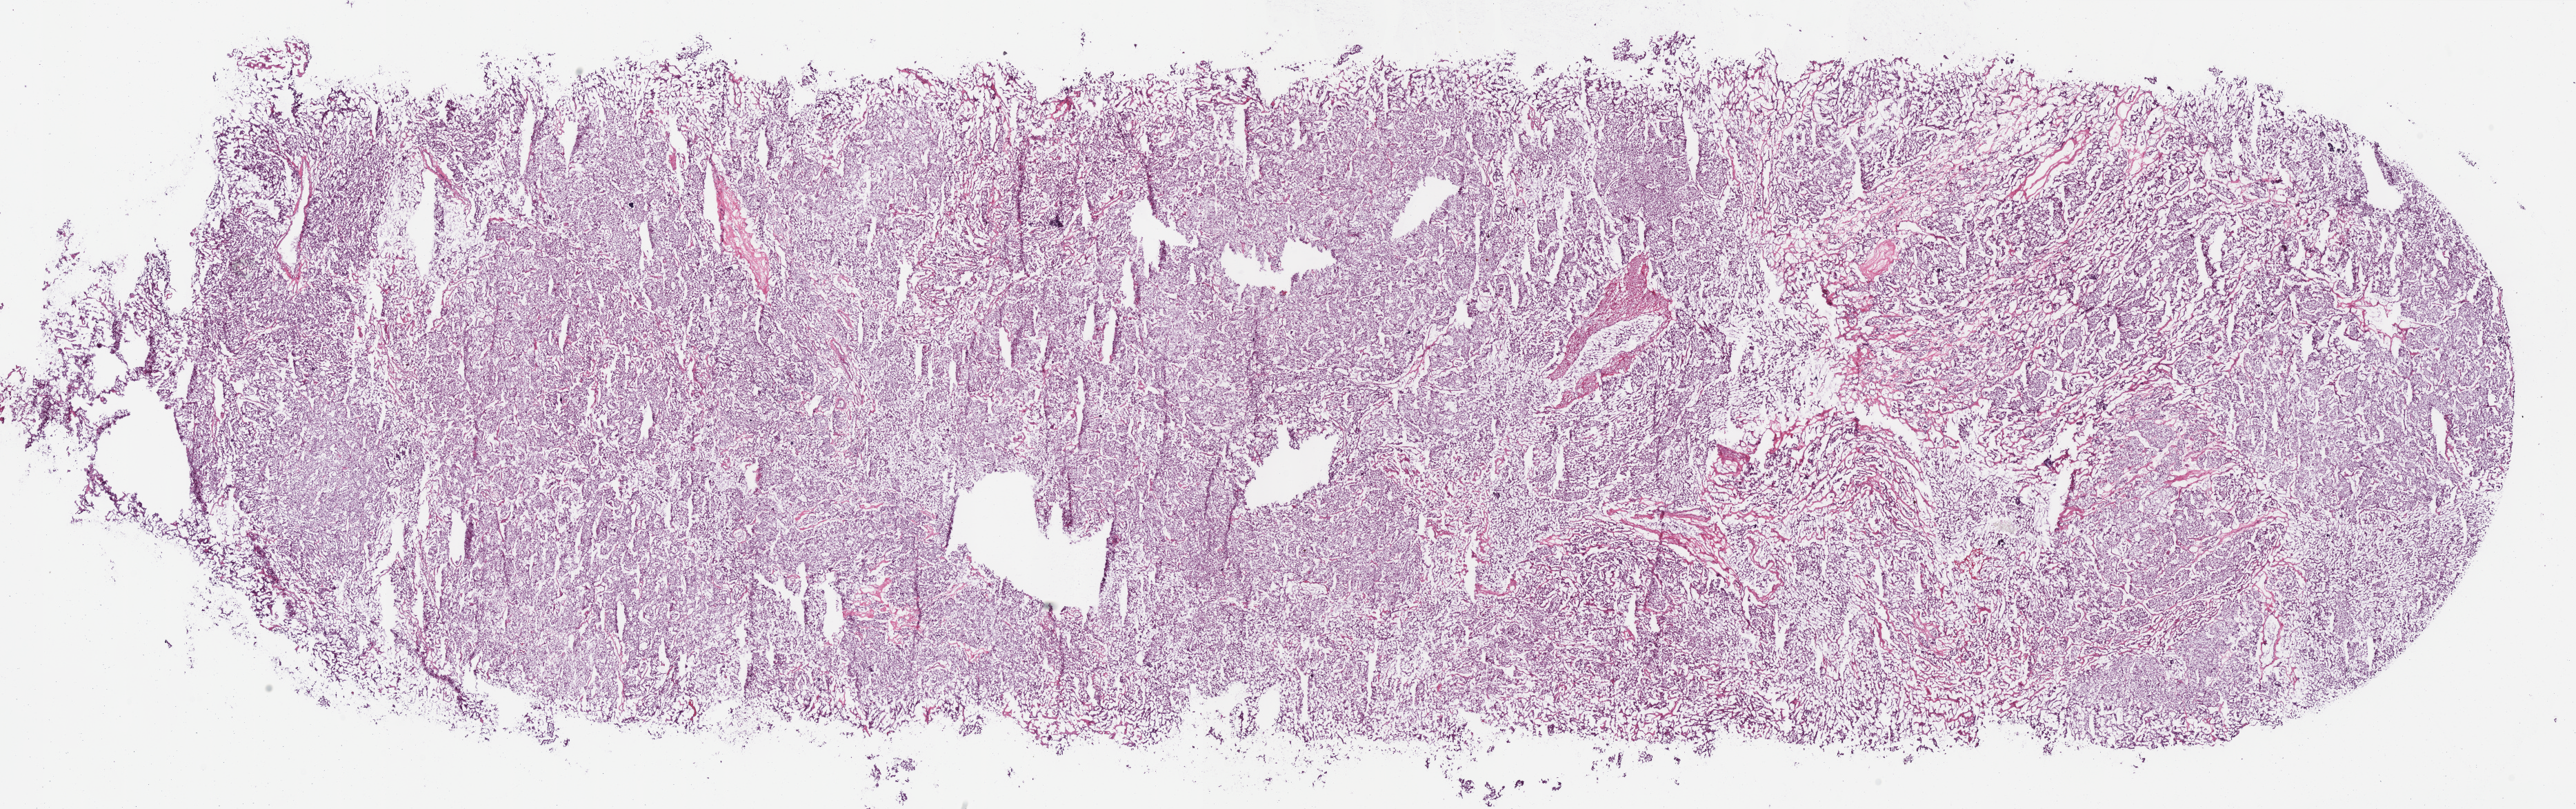
Hematoxylin and eosin (H&E) stained whole-slide image, shown as a low-resolution overview of the whole scanned area (about 29.4 x 9.2 mm), frozen section from the bottom of the tissue portion, kidney, primary tumour sample. Male patient; age at initial diagnosis 42 years. Pathologist review of this section (percent, as recorded): tumour cells 90%, tumour nuclei 90%, normal cells 0%, stromal cells 10%, necrosis 0%.
AJCC pathologic stage: II (7th edition). Pathologic diagnosis: Renal cell carcinoma, chromophobe type.